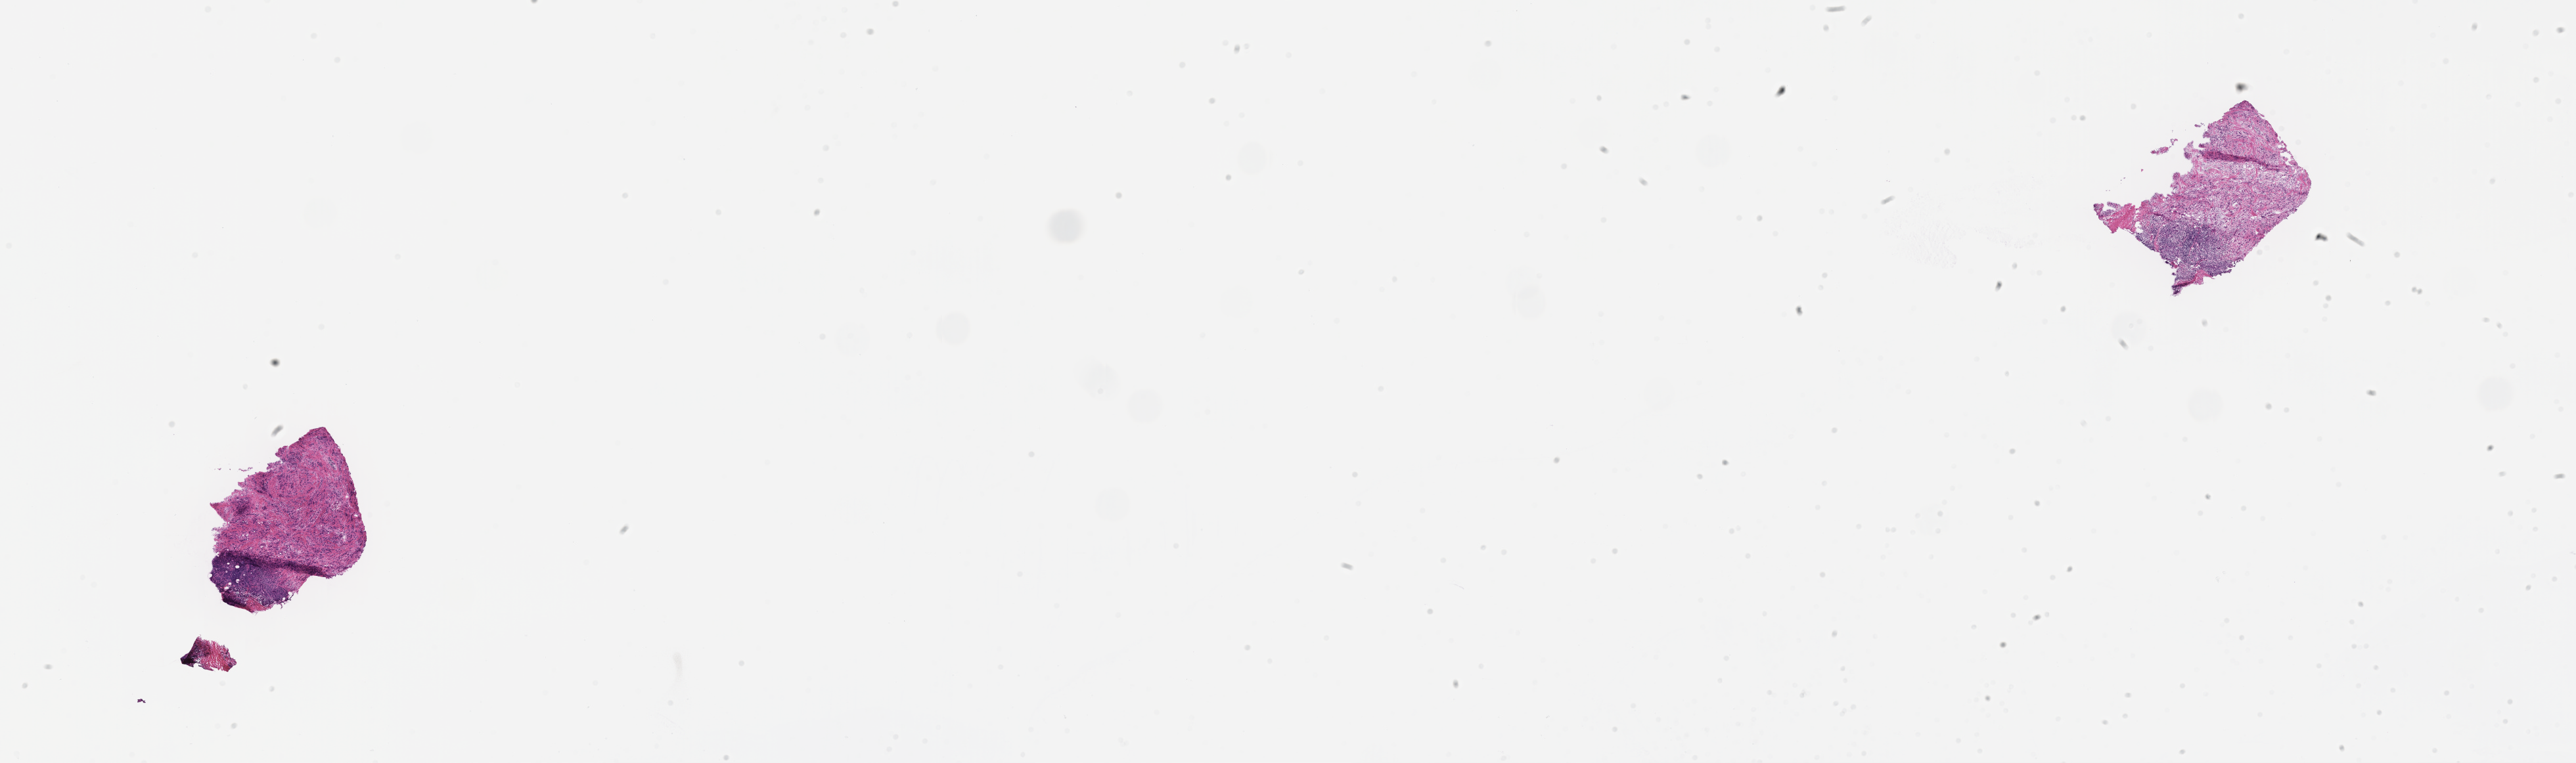
Whole-slide image, haematoxylin and eosin stain, a low-resolution overview of the entire scanned area, about 31.6 x 9.4 mm; frozen section; primary tumor; anatomic site: breast (left). Patient: female, age at initial diagnosis 60 years. Pathologist review of this section (percent, as recorded): tumor cells 30%, tumor nuclei 30%, stromal cells 50%, necrosis 0%, normal cells 20%. Infiltration values recorded for this section: lymphocyte infiltration 5%, monocyte infiltration 2%, neutrophil infiltration 0%.
- histologic diagnosis: Infiltrating duct carcinoma, NOS